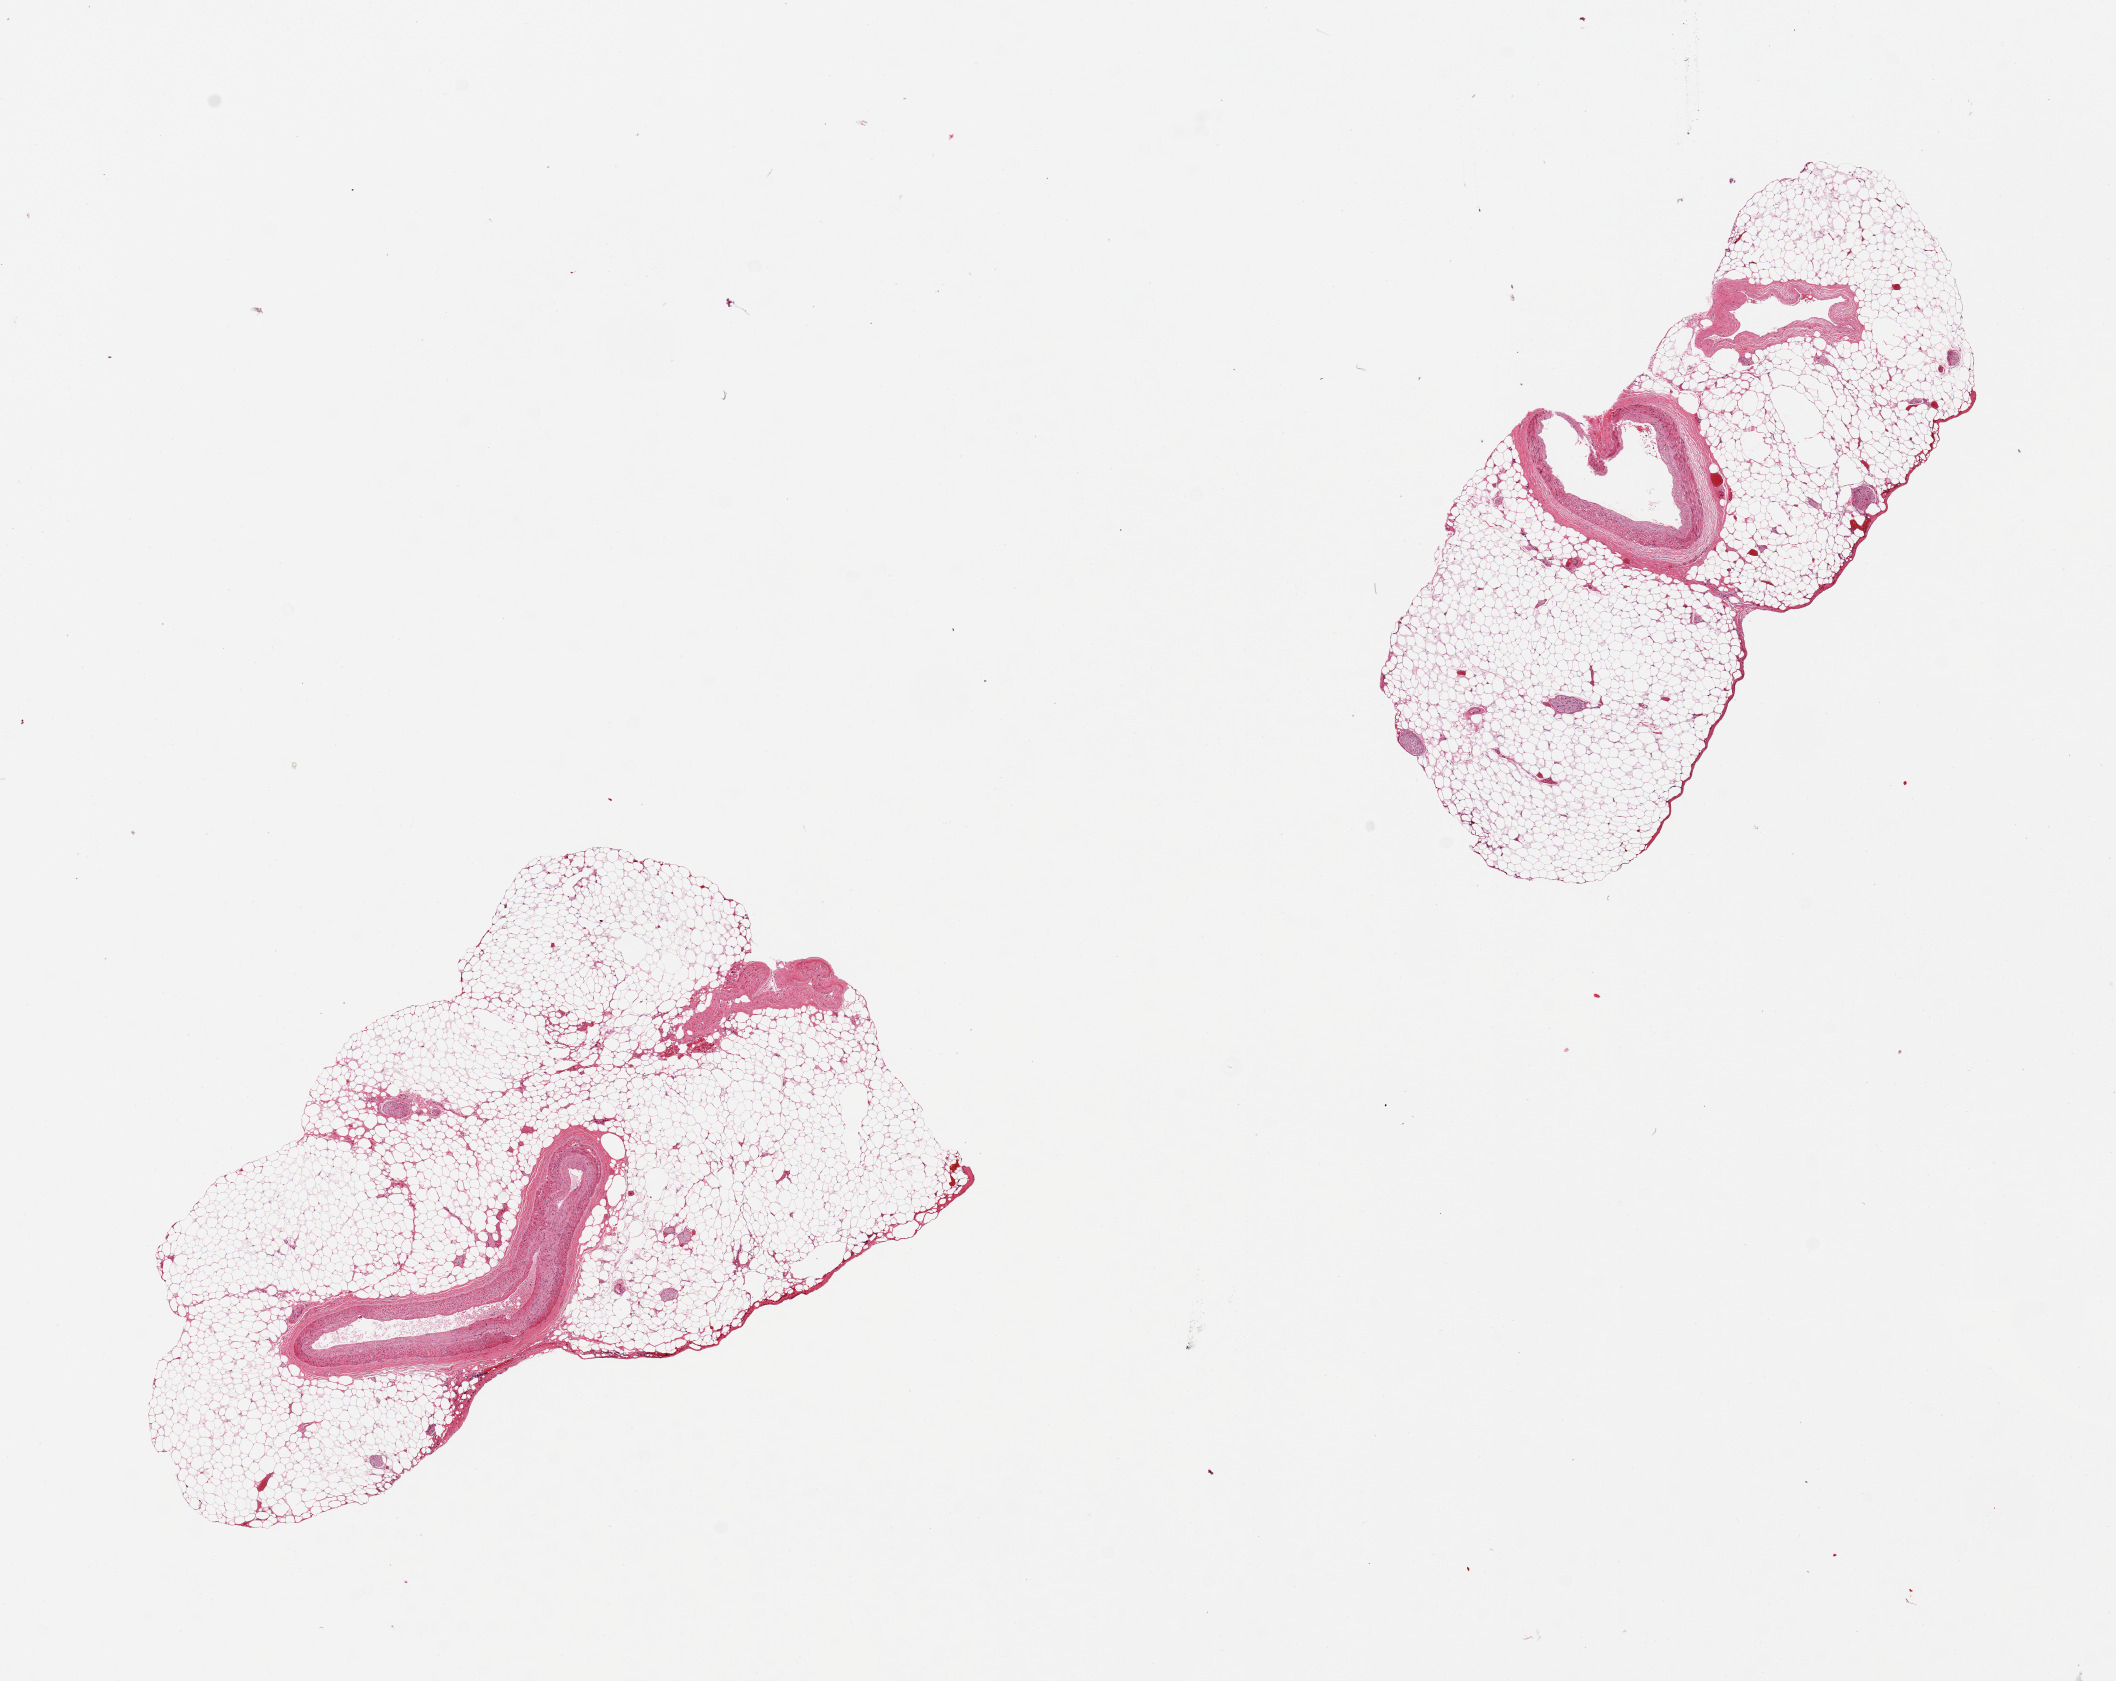
Whole-slide image, hematoxylin and eosin (H&E) stain — shown as a low-resolution overview of the whole scanned area (about 16.7 x 13.3 mm), PAXgene-fixed, paraffin-embedded tissue, section of coronary artery (target tissue), donor tissue sample. Donor: female.
Review note (as recorded): 2 pieces, both with 80% fat.